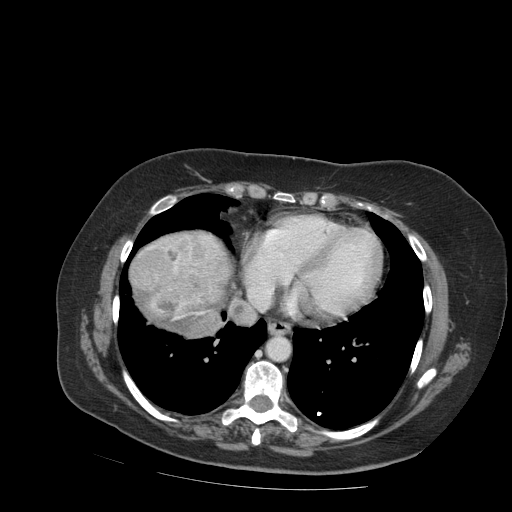
Contrast-enhanced abdominal CT (liver protocol), one axial slice; position 87 of 99 along the scan axis; 140 kVp; soft-tissue window (W 400 / L 40 HU); 2.5 mm slice thickness; 512 × 512 image matrix, field of view 400 × 400 mm. From the clinical record (not read from this slice): diagnosis: hepatocellular carcinoma (patient treated with transarterial chemoembolisation; whether this scan precedes or follows treatment is not stated here); TNM stage (as recorded): Stage-IVB; Child-Pugh class: A; tumour differentiation: moderately differentiated; tumour nodularity: uninodular.
Structures marked on this image (semi-automatically segmented with operator editing):
- liver parenchyma outside the tumour (the mass and vessels are separate outlines, so this box may not span the whole liver): bounding box [x1, y1, x2, y2] px = [128, 230, 230, 336]
- mass: [135, 244, 233, 331]
- liver vessels: [149, 247, 152, 249]